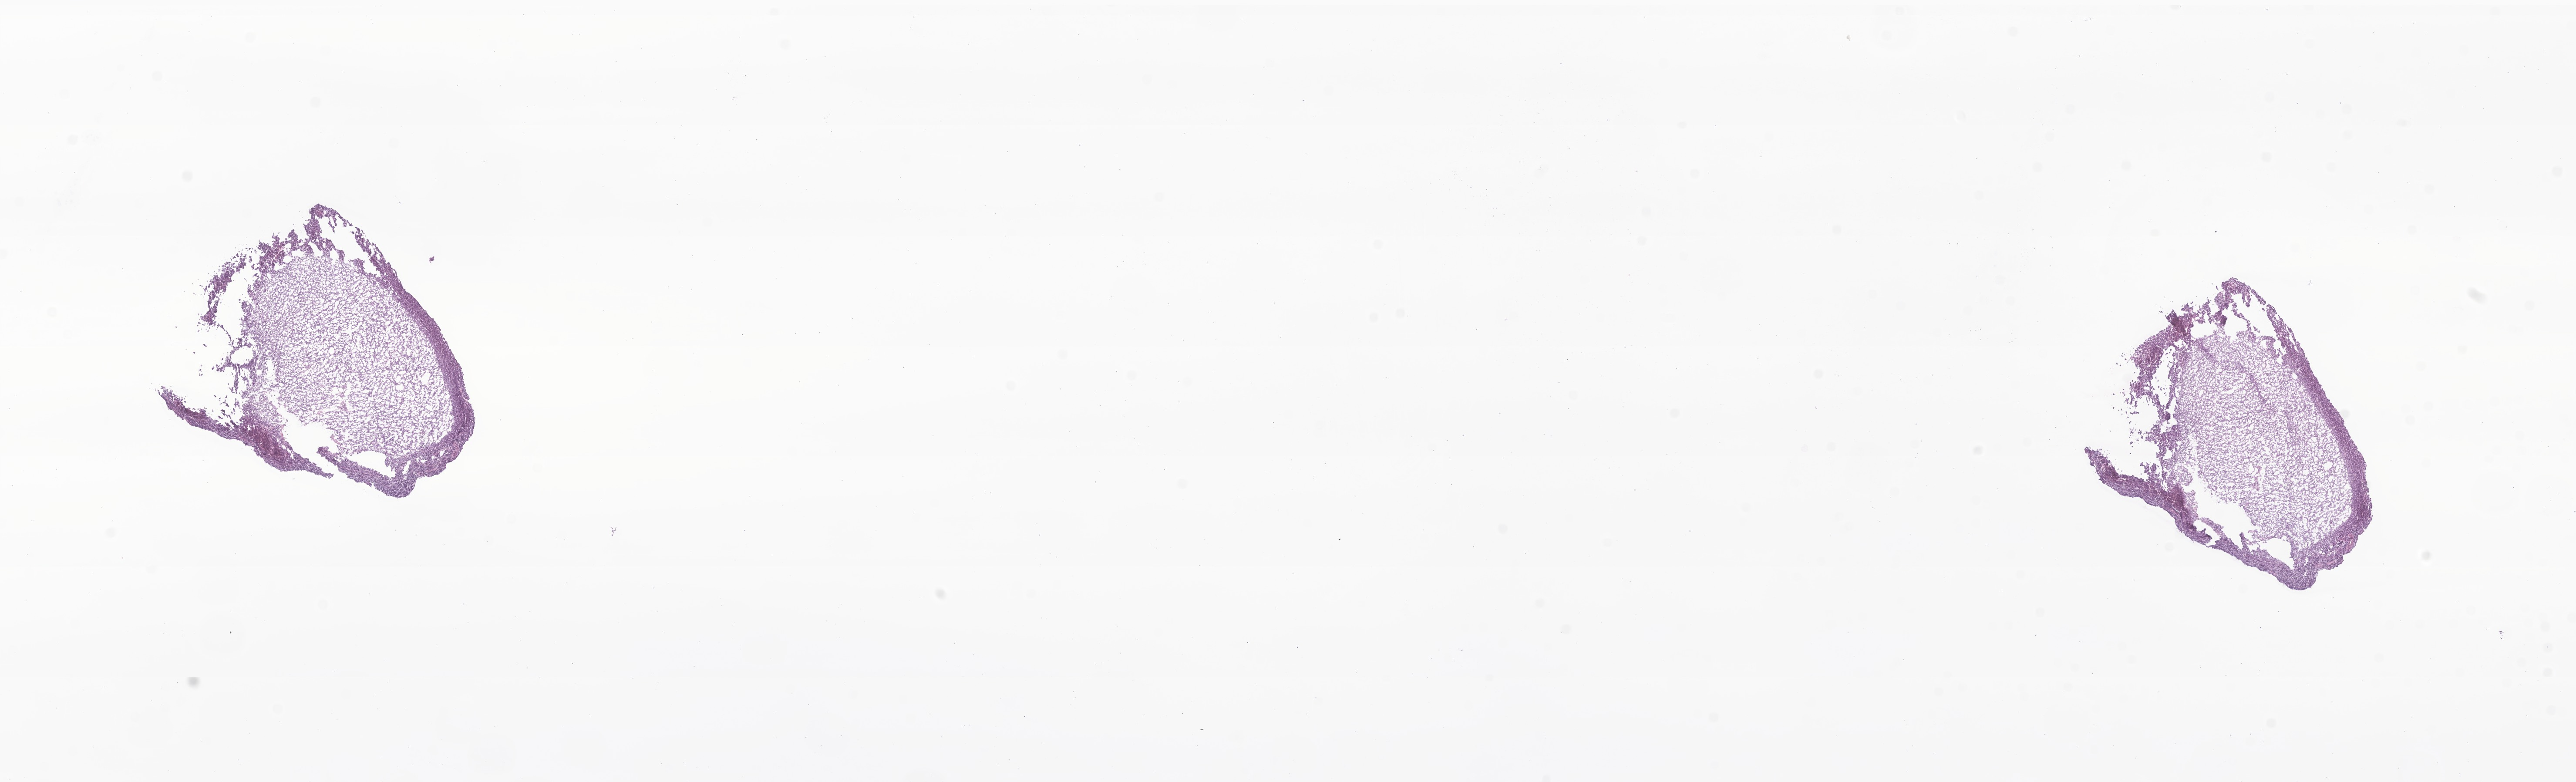
Hematoxylin and eosin (H&E) whole-slide image of tumor tissue from the cauda equina — whole scanned area (about 24.9 x 7.6 mm) shown as a low-resolution overview, frozen section (OCT-embedded). Patient: male, age 172 months (14 years 4 months).
Recorded diagnosis: Atypical teratoid/rhabdoid tumor.